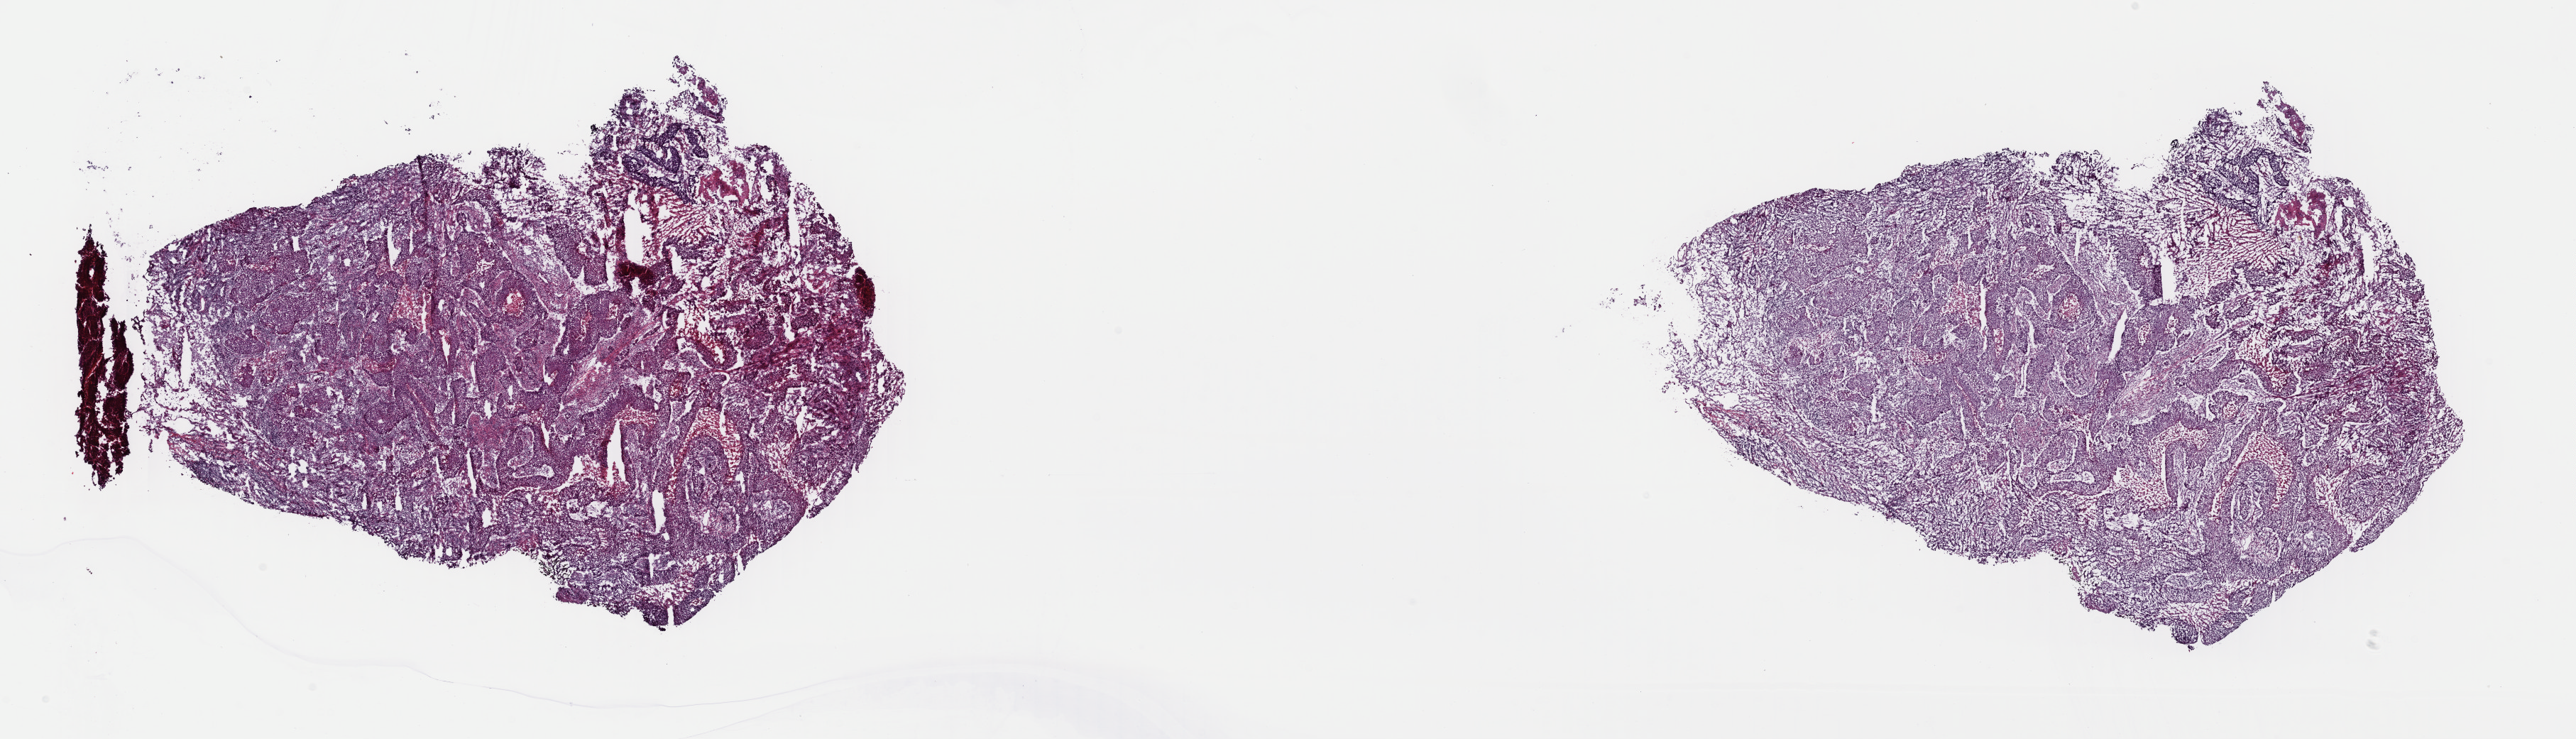
H&E-stained whole-slide image — whole scanned area (about 28.6 x 8.2 mm, acquisition: 40x scan) shown as a low-resolution overview. Frozen section from the top of the tissue portion. Sample: primary tumour, lung. Male patient; age at initial diagnosis 63 years. Slide review estimates, as recorded: tumour cells 80%, tumour nuclei 95%, normal cells 0%, stromal cells 5%, necrosis 15%. Inflammatory infiltration, as recorded: lymphocyte infiltration 0%, monocyte infiltration 0%, neutrophil infiltration 0%.
• AJCC pathologic stage: IIB (6th edition)
• pathologic diagnosis: Squamous cell carcinoma, NOS